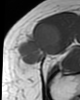
MRI of an extremity soft-tissue mass, one axial slice; slice 18 of 46 in the series (ordered by position); MR volume resampled by the dataset authors to the PET/CT grid (not the native acquisition matrix); 3.27 mm slice thickness; 80 × 100 image matrix, field of view 78 × 98 mm. Female patient. From the clinical record (not read from this slice): histological type: synovial sarcoma; grade: intermediate; site of the primary tumour: right thigh.
Structures marked on this image (expert contour drawn on MRI and transferred to this co-registered scan by the dataset authors):
- gross tumour volume including surrounding oedema: bounding box <14,23,61,66> (left, top, right, bottom; pixels)
- gross tumour volume (mass): <14,23,61,66>